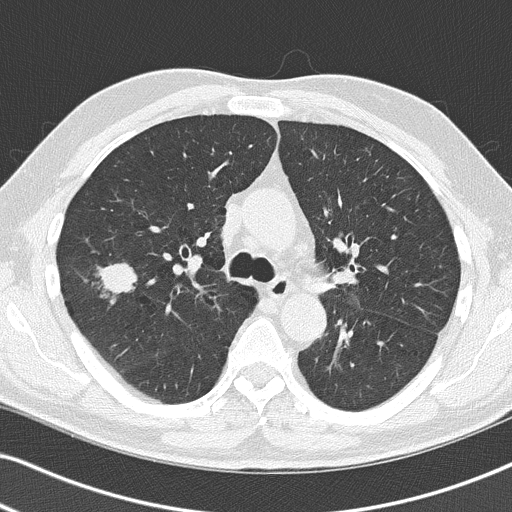
Axial slice from a low-dose chest CT screening exam. Baseline annual screen. Lung window (W 1500 / L -600 HU). Lung (sharp) reconstruction kernel (B50f). 120 kVp. Slice 55 of 140 in the series. 512 × 512 image matrix. Male, age 67 years at enrolment. Former smoker at enrolment.
Expert reader's lesion annotation, bounding box <73,255,149,316> (left, top, right, bottom; pixels). The exam's reader record, not a measurement of the box and not confirmed to be the same lesion: non-calcified nodule or mass ≥4 mm, right upper lobe, 26 × 24 mm, spiculated (stellate) margins, soft tissue attenuation. Participant outcome: lung cancer diagnosed 49 days after this screen — squamous cell carcinoma, NOS, right upper lobe, poorly differentiated (G3), stage IA (AJCC 6th edition), 27 mm at pathology.